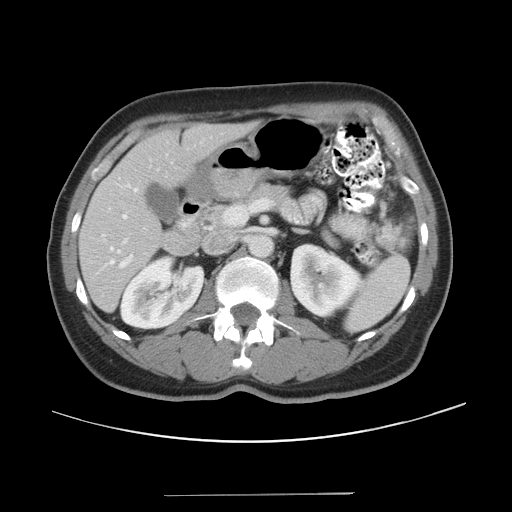
Contrast-enhanced abdominal CT, one axial slice; position 19 of 43 along the scan axis; intravenous contrast given; soft-tissue window (W 400 / L 40 HU); 512 × 512 image matrix, field of view 409 × 409 mm. Male patient, age 65 years. Case-level facts recorded for this patient, not image findings: diagnosis: colorectal cancer liver metastases, imaged before liver resection; multiple liver metastases: no; largest metastasis: 3.8 cm.
Annotated regions visible in this slice (outlined manually by an expert reader):
- hepatic veins: bounding box <108,183,139,264> (left, top, right, bottom; pixels)
- liver: <81,124,247,310>
- planned liver remnant (the part of the liver to remain after resection): <81,124,247,310>
- portal vein (with intrahepatic branches): <102,214,133,264>